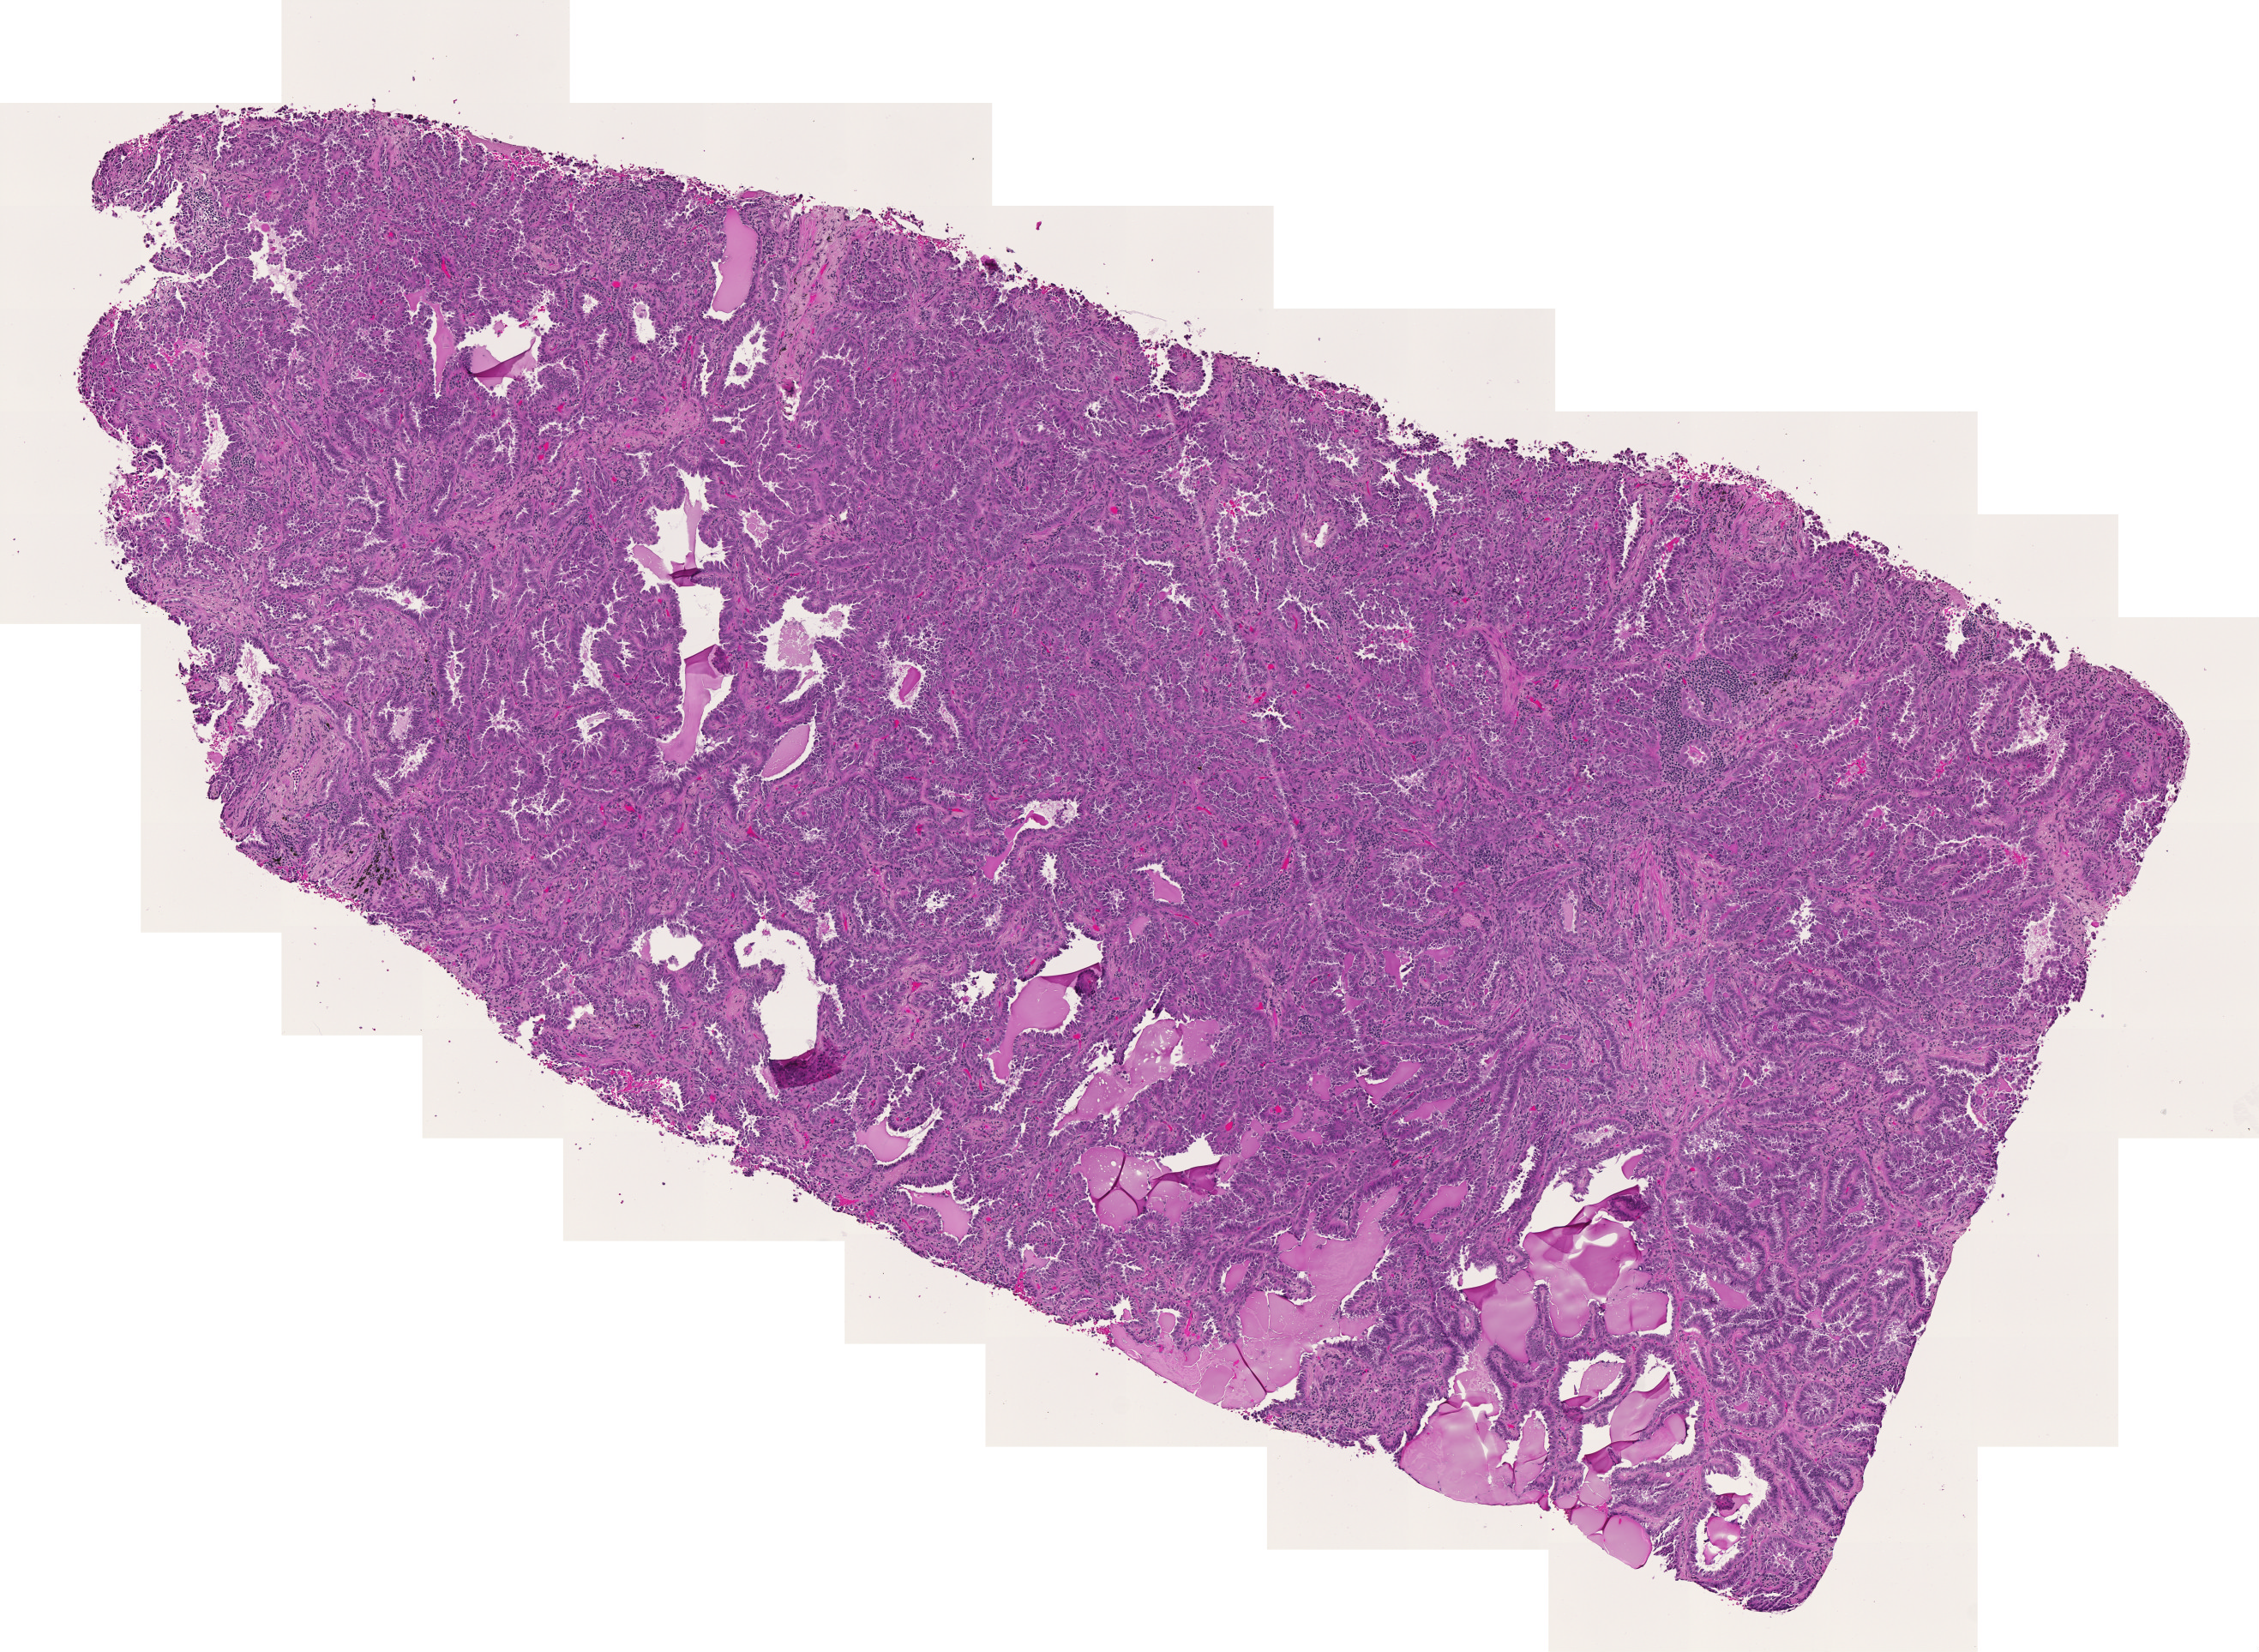
Digitized H&E-stained tissue section (whole slide), shown as a low-resolution overview of the whole scanned area (about 6.8 x 5.0 mm). Lung, tumour tissue. Male, 73 y/o. Histologic grade: G1 (well differentiated).
* AJCC pathologic stage: IA
* histologic diagnosis: Adenocarcinoma, NOS